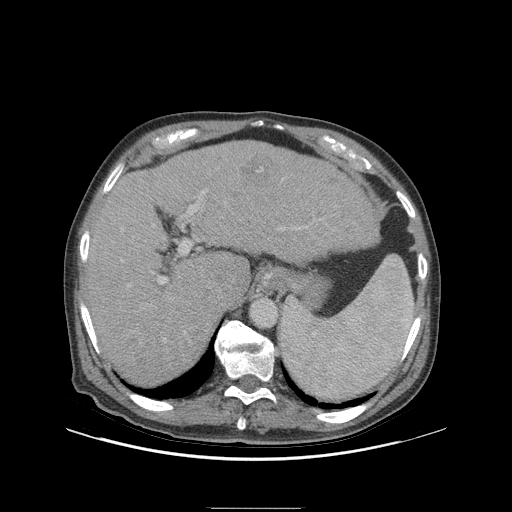
Contrast-enhanced abdominal CT (liver protocol), one axial slice. Slice 70 of 105 in the series (ordered by position). 140 kVp. Soft-tissue window (W 400 / L 40 HU). 2.5 mm slice thickness. 512 × 512 image matrix, field of view 440 × 440 mm. Case-level facts recorded for this patient, not image findings: diagnosis: hepatocellular carcinoma (patient treated with transarterial chemoembolisation; whether this scan precedes or follows treatment is not stated here); TNM stage (as recorded): Stage-I; Child-Pugh class: A; tumour nodularity: uninodular; tumour size: 5.1 cm.
Annotated regions visible in this slice (semi-automatic segmentation, software-assisted and operator-edited):
- liver parenchyma outside the tumour (the mass and vessels are separate outlines, so this box may not span the whole liver): bounding box [x1, y1, x2, y2] px = [84, 140, 378, 386]
- mass: [240, 152, 271, 188]
- liver vessels: [94, 179, 321, 352]